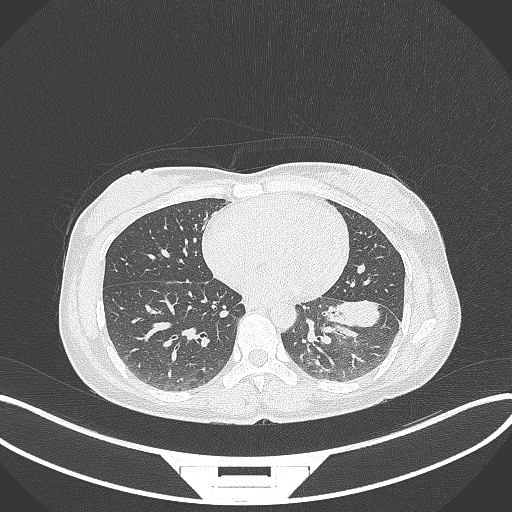
Chest CT, one axial slice; position 27 of 244 along the scan axis; reconstruction kernel B70f; 120 kVp; lung window (W 1500 / L -600 HU); 512 × 512 image matrix, field of view 400 × 400 mm. Female patient, age 41 years. From the clinical record (not read from this slice): clinical TNM (as recorded): T2a N3 M1b.
Outlined on this slice (bounding box drawn by a radiologist):
- lung tumour (recorded histology: adenocarcinoma): box from (x=323, y=297) to (x=387, y=332) px